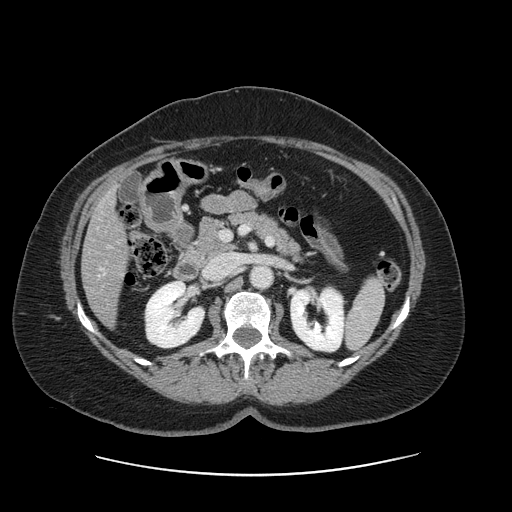
Contrast-enhanced abdominal CT, one axial slice. Position 62 of 161 along the scan axis. 120 kVp. Intravenous contrast given. Soft-tissue window (W 400 / L 40 HU). 2.5 mm slice thickness. 512 × 512 image matrix, field of view 398 × 398 mm. Female patient, age 62 years. Case-level facts recorded for this patient, not image findings: diagnosis: colorectal cancer liver metastases, imaged before liver resection; multiple liver metastases: no; largest metastasis: 2.5 cm; disease in both lobes: no.
Outlined on this slice (manually delineated by an expert):
- liver: box from (x=83, y=191) to (x=128, y=324) px